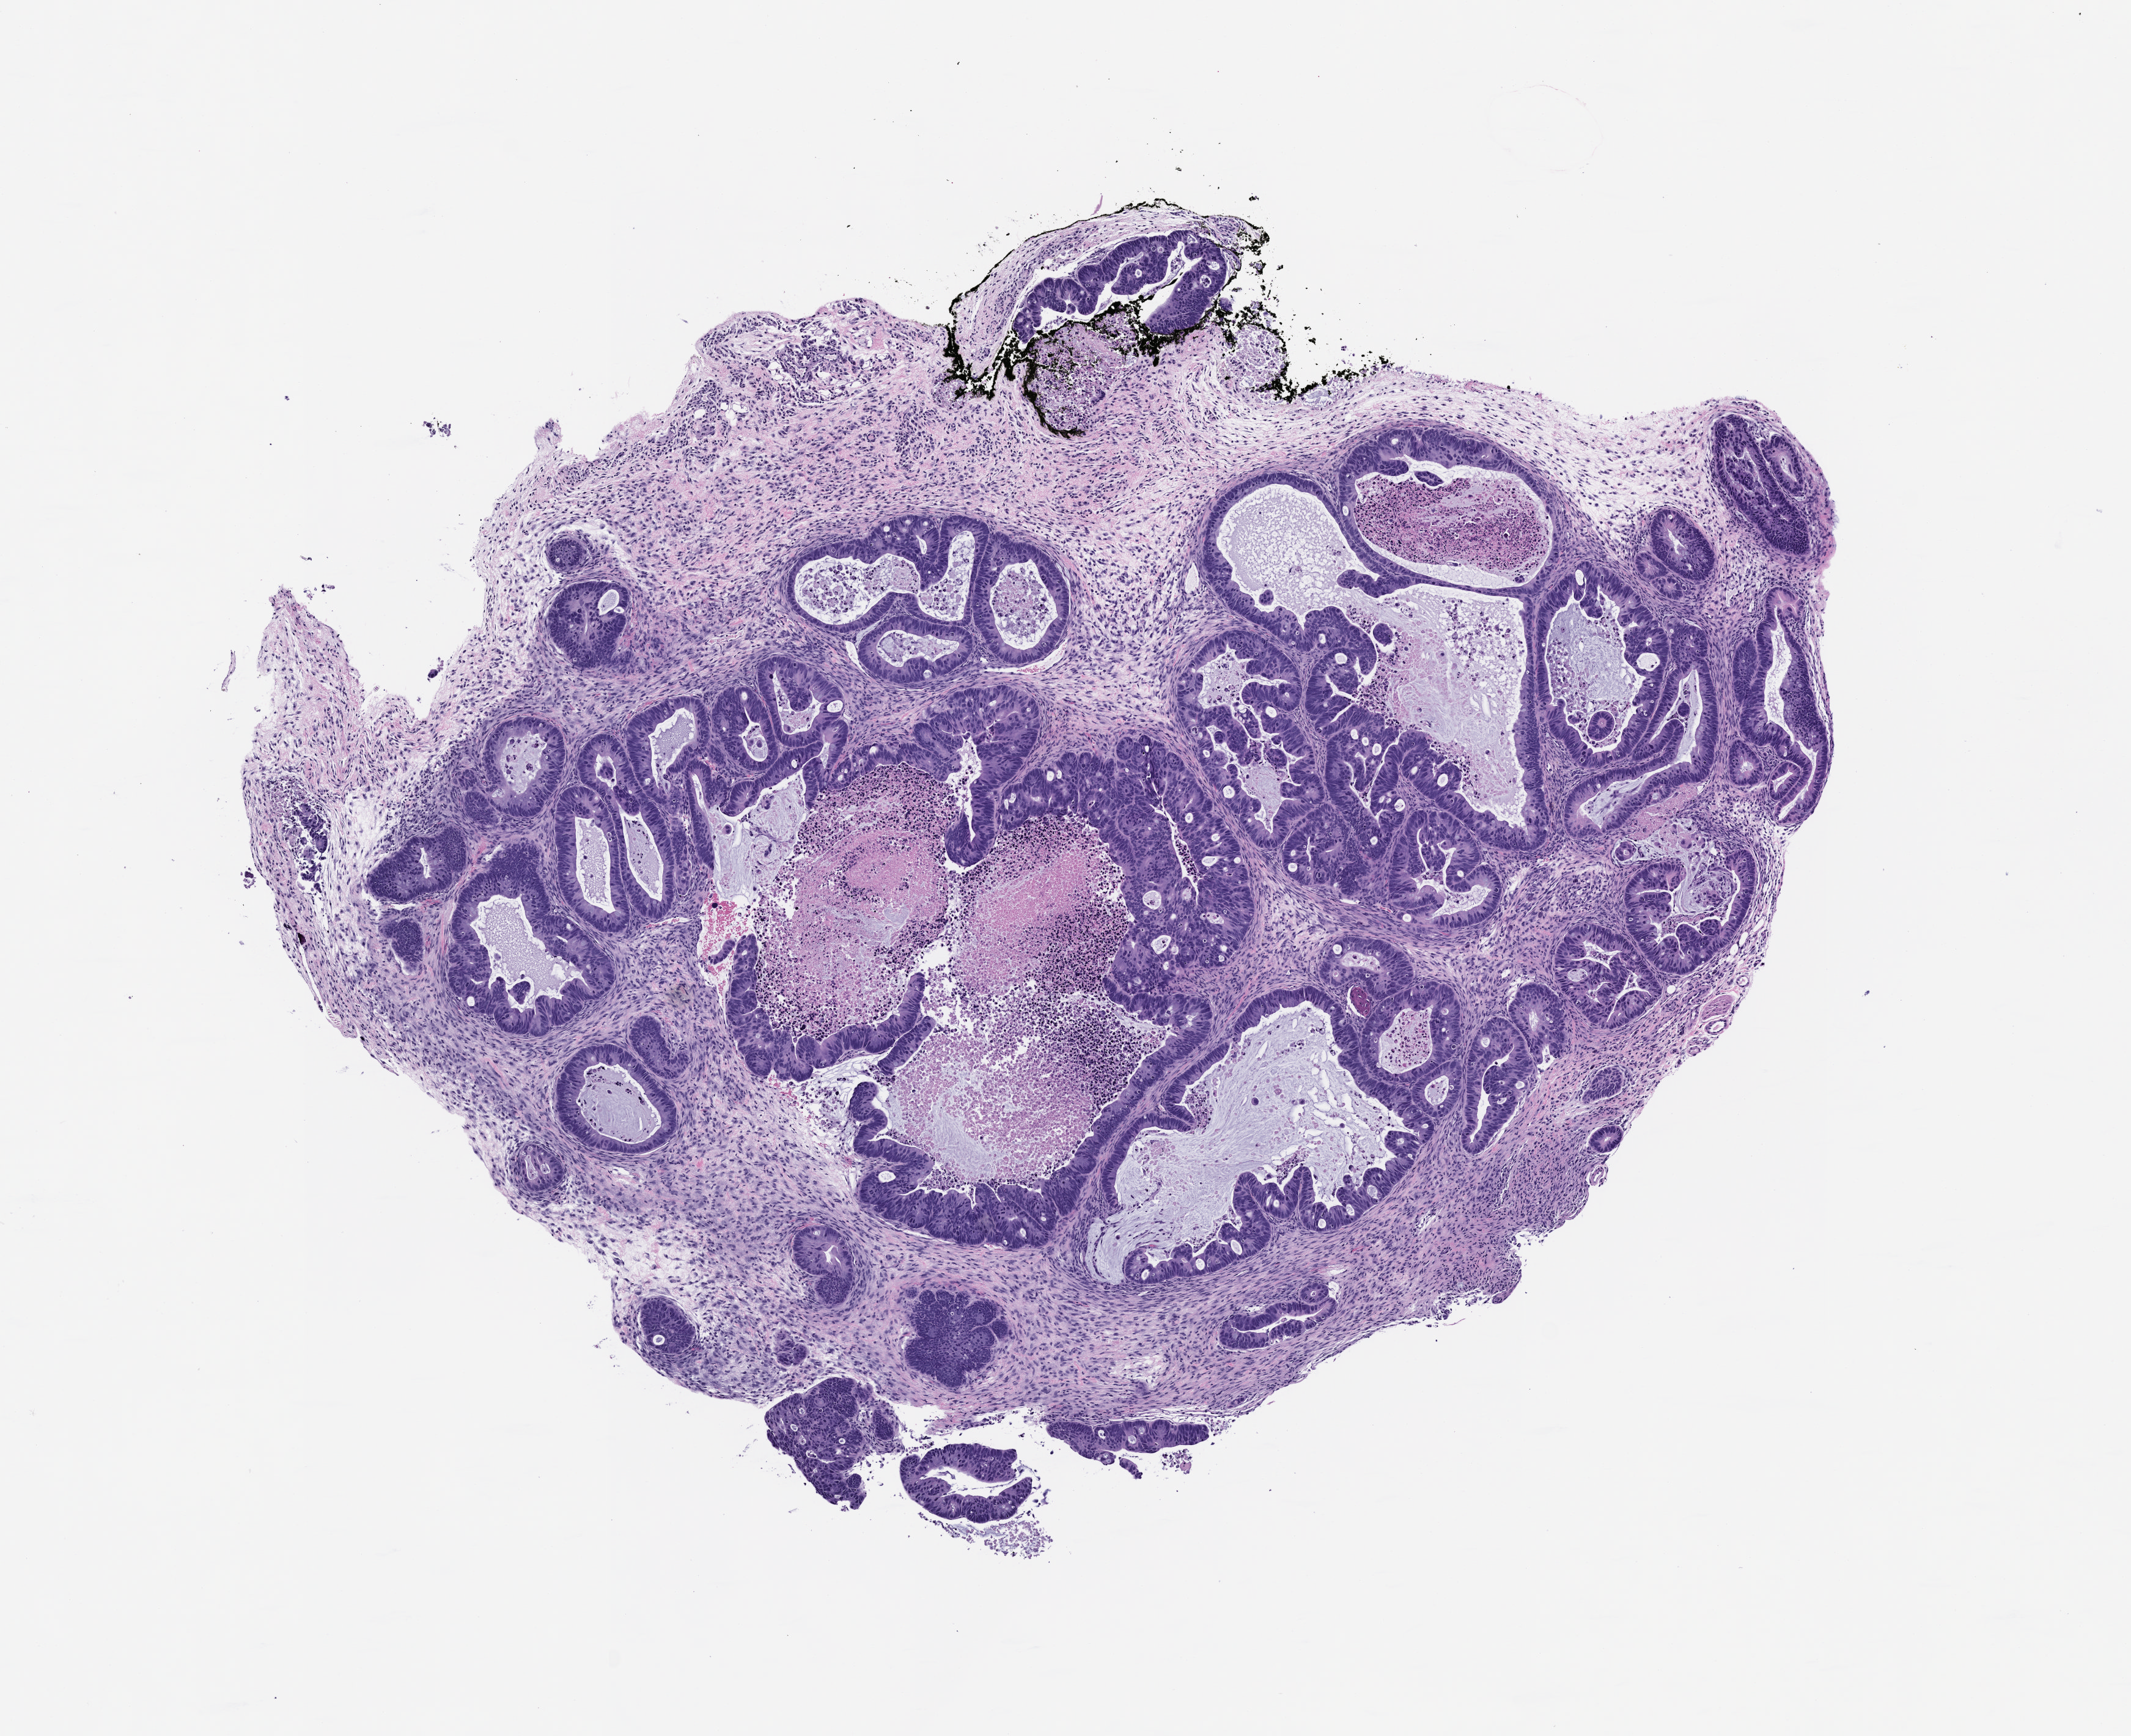
Whole-slide image, haematoxylin and eosin: patient-derived xenograft (human tumor grown in a mouse), passage 0, a low-resolution overview of the entire scanned area, about 7.0 x 5.7 mm. Formalin-fixed paraffin-embedded section. Tumor site category: gastrointestinal tract.
- originating patient diagnosis: Colorectal Carcinoma